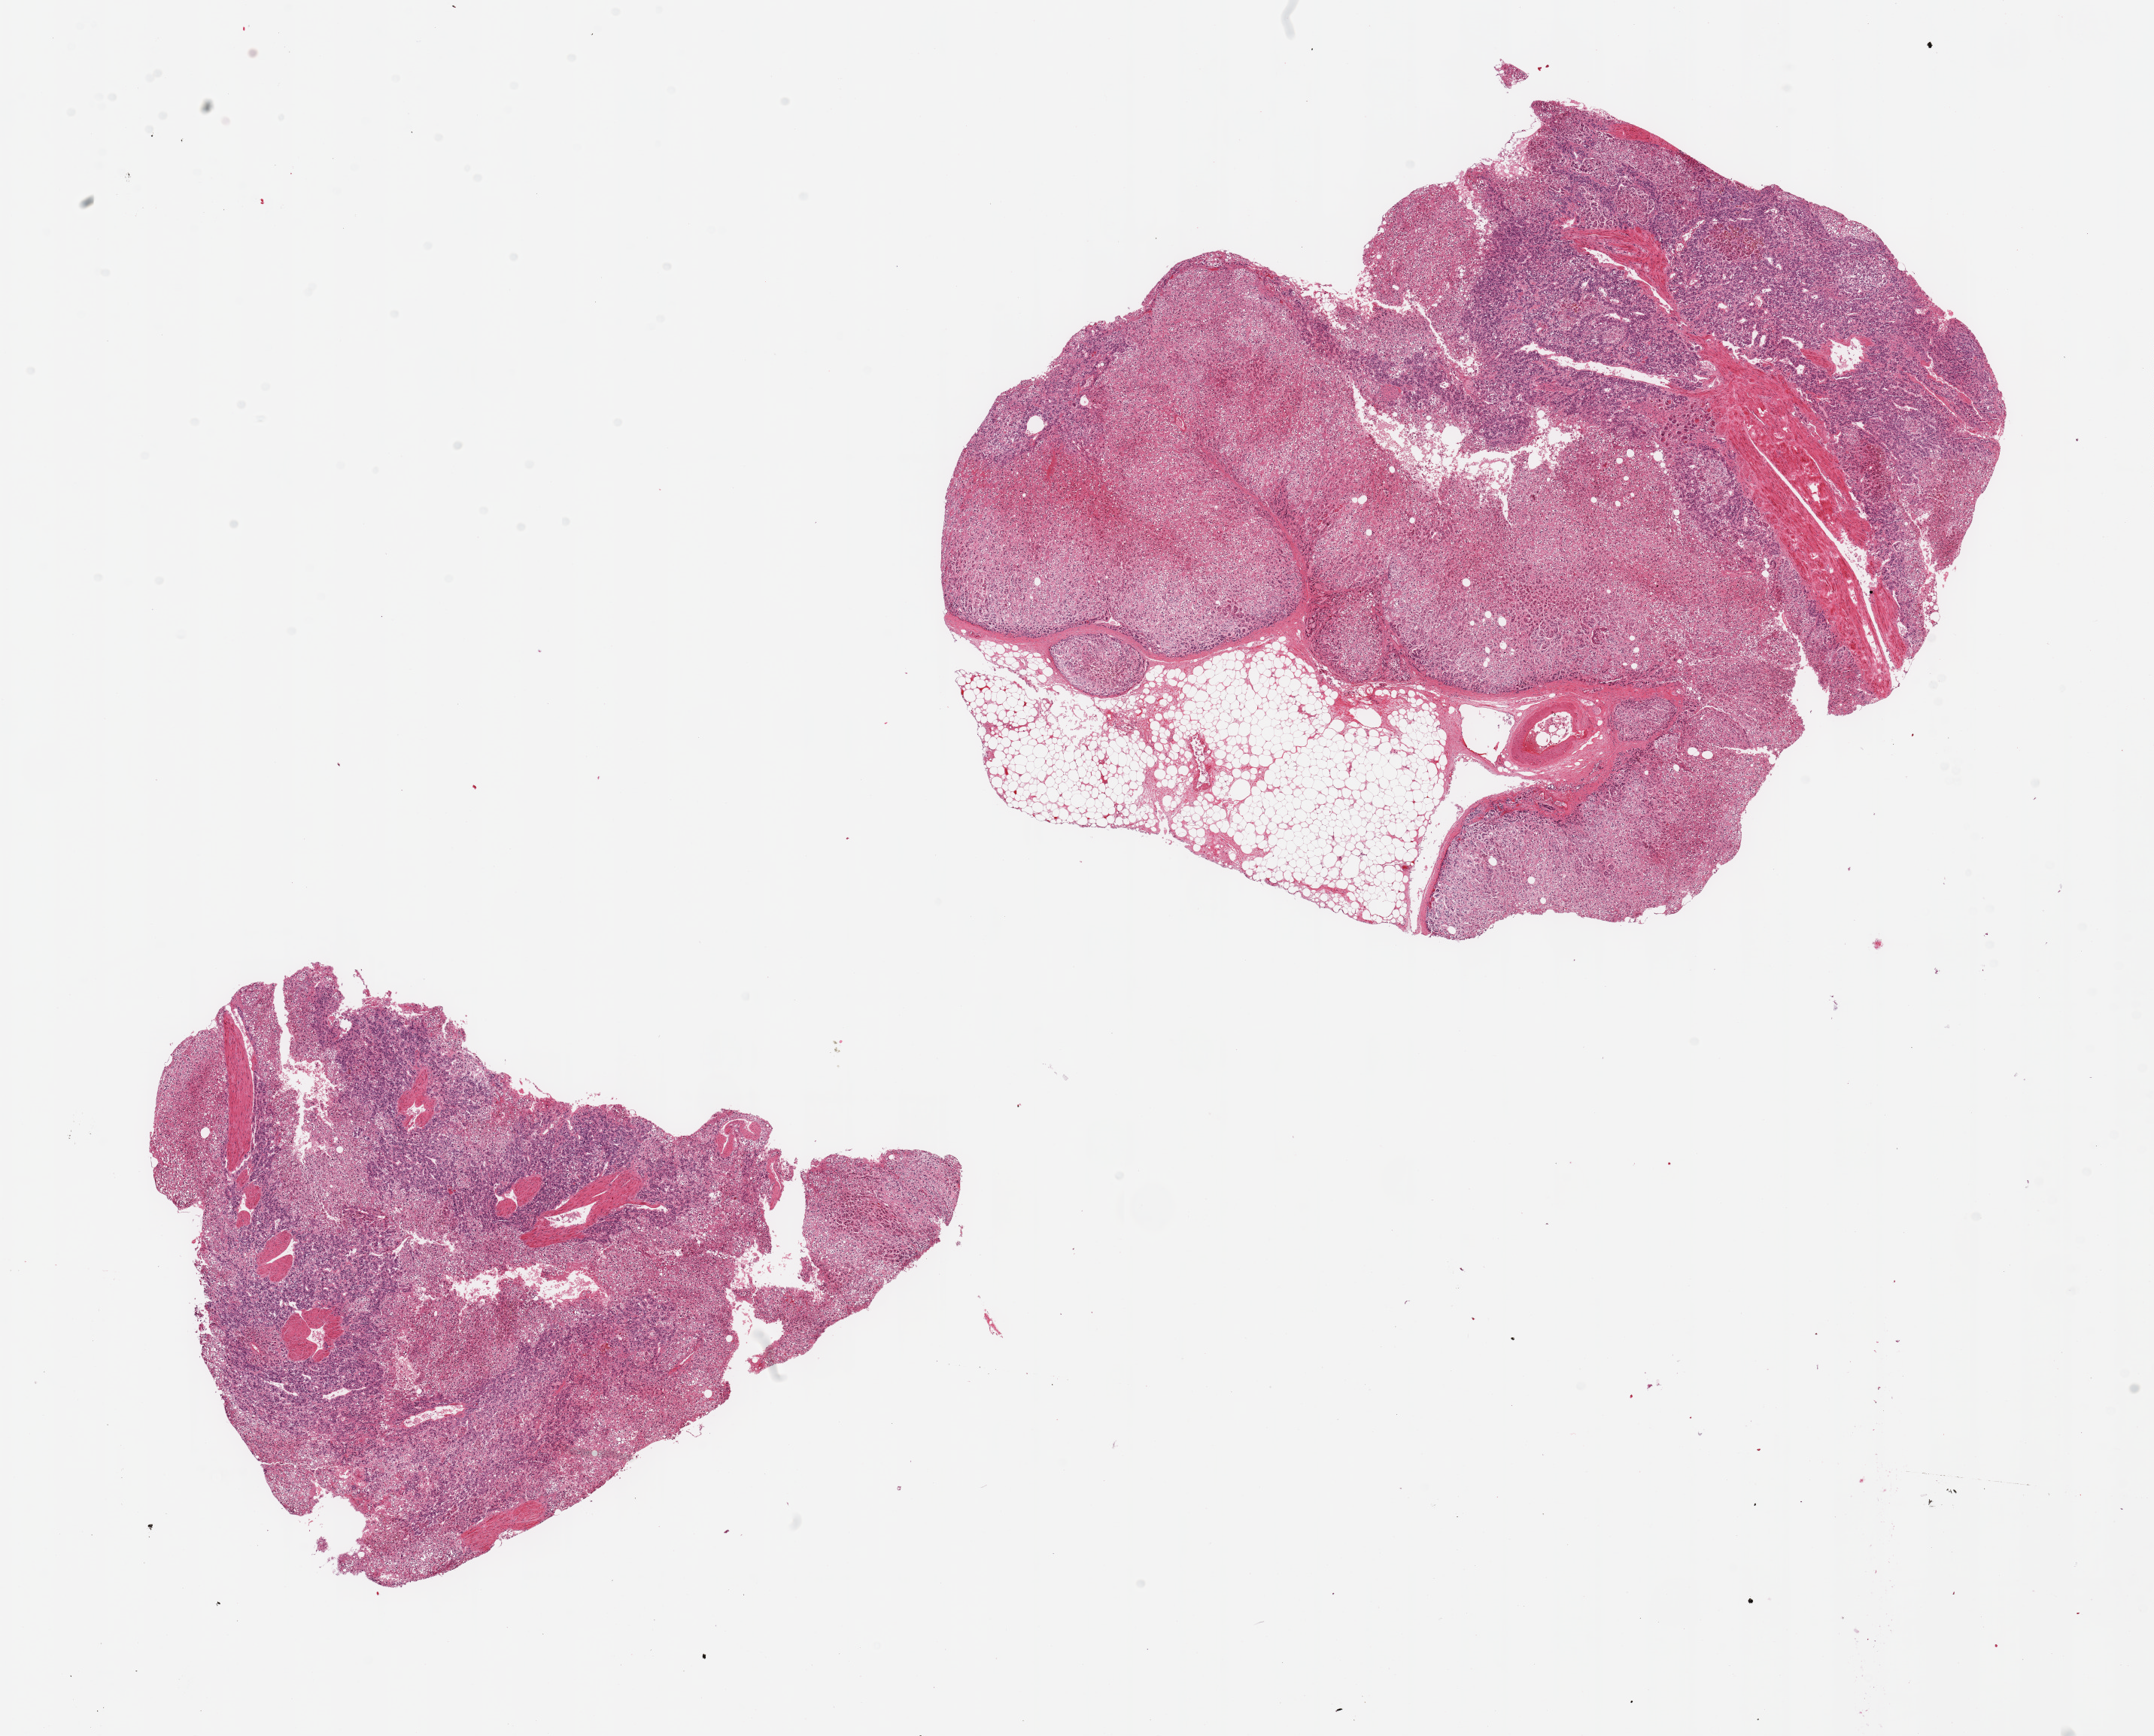
Digitized H&E-stained section, whole scanned area (about 22.6 x 18.3 mm) shown as a low-resolution overview. PAXgene-fixed paraffin-embedded (PFPE) section. Target tissue: adrenal gland. Donor tissue sample. Donor sex: male.
* reviewer comment on this tissue sample: 2 pieces; adrenal cortex and medulla, one piece with ~20% external fat